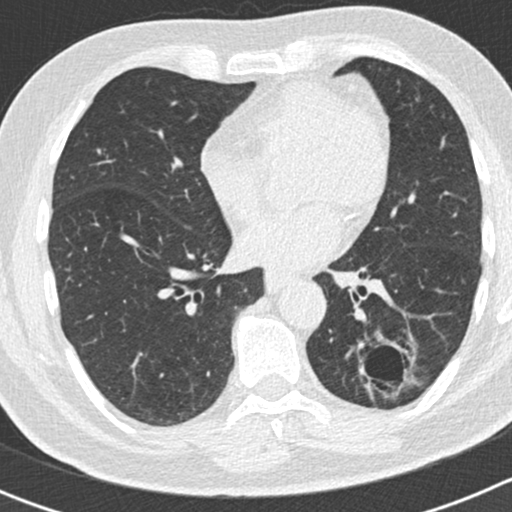
Axial slice from a low-dose chest CT screening exam, second annual screen, lung window (W 1500 / L -600 HU), 2 mm slice thickness, 120 kVp, slice 95 of 186 in the series. Male participant, aged 66 years at enrolment. Former smoker at enrolment.
Expert reader's lesion annotation, bounding box <348,330,414,404> (left, top, right, bottom; pixels). Reader record for this screening exam (exam-level; its link to the box is not recorded): non-calcified nodule or mass ≥4 mm, left lower lobe, 50 × 33 mm, smooth margins, pre-existing on the prior screen: yes; interval growth: yes. Official screen result: positive, other. Lung cancer was diagnosed 440 days after this screen (after the third annual screen): adenocarcinoma, NOS, left lower lobe, poorly differentiated (G3), stage IB (AJCC 6th edition), 38 mm at pathology.